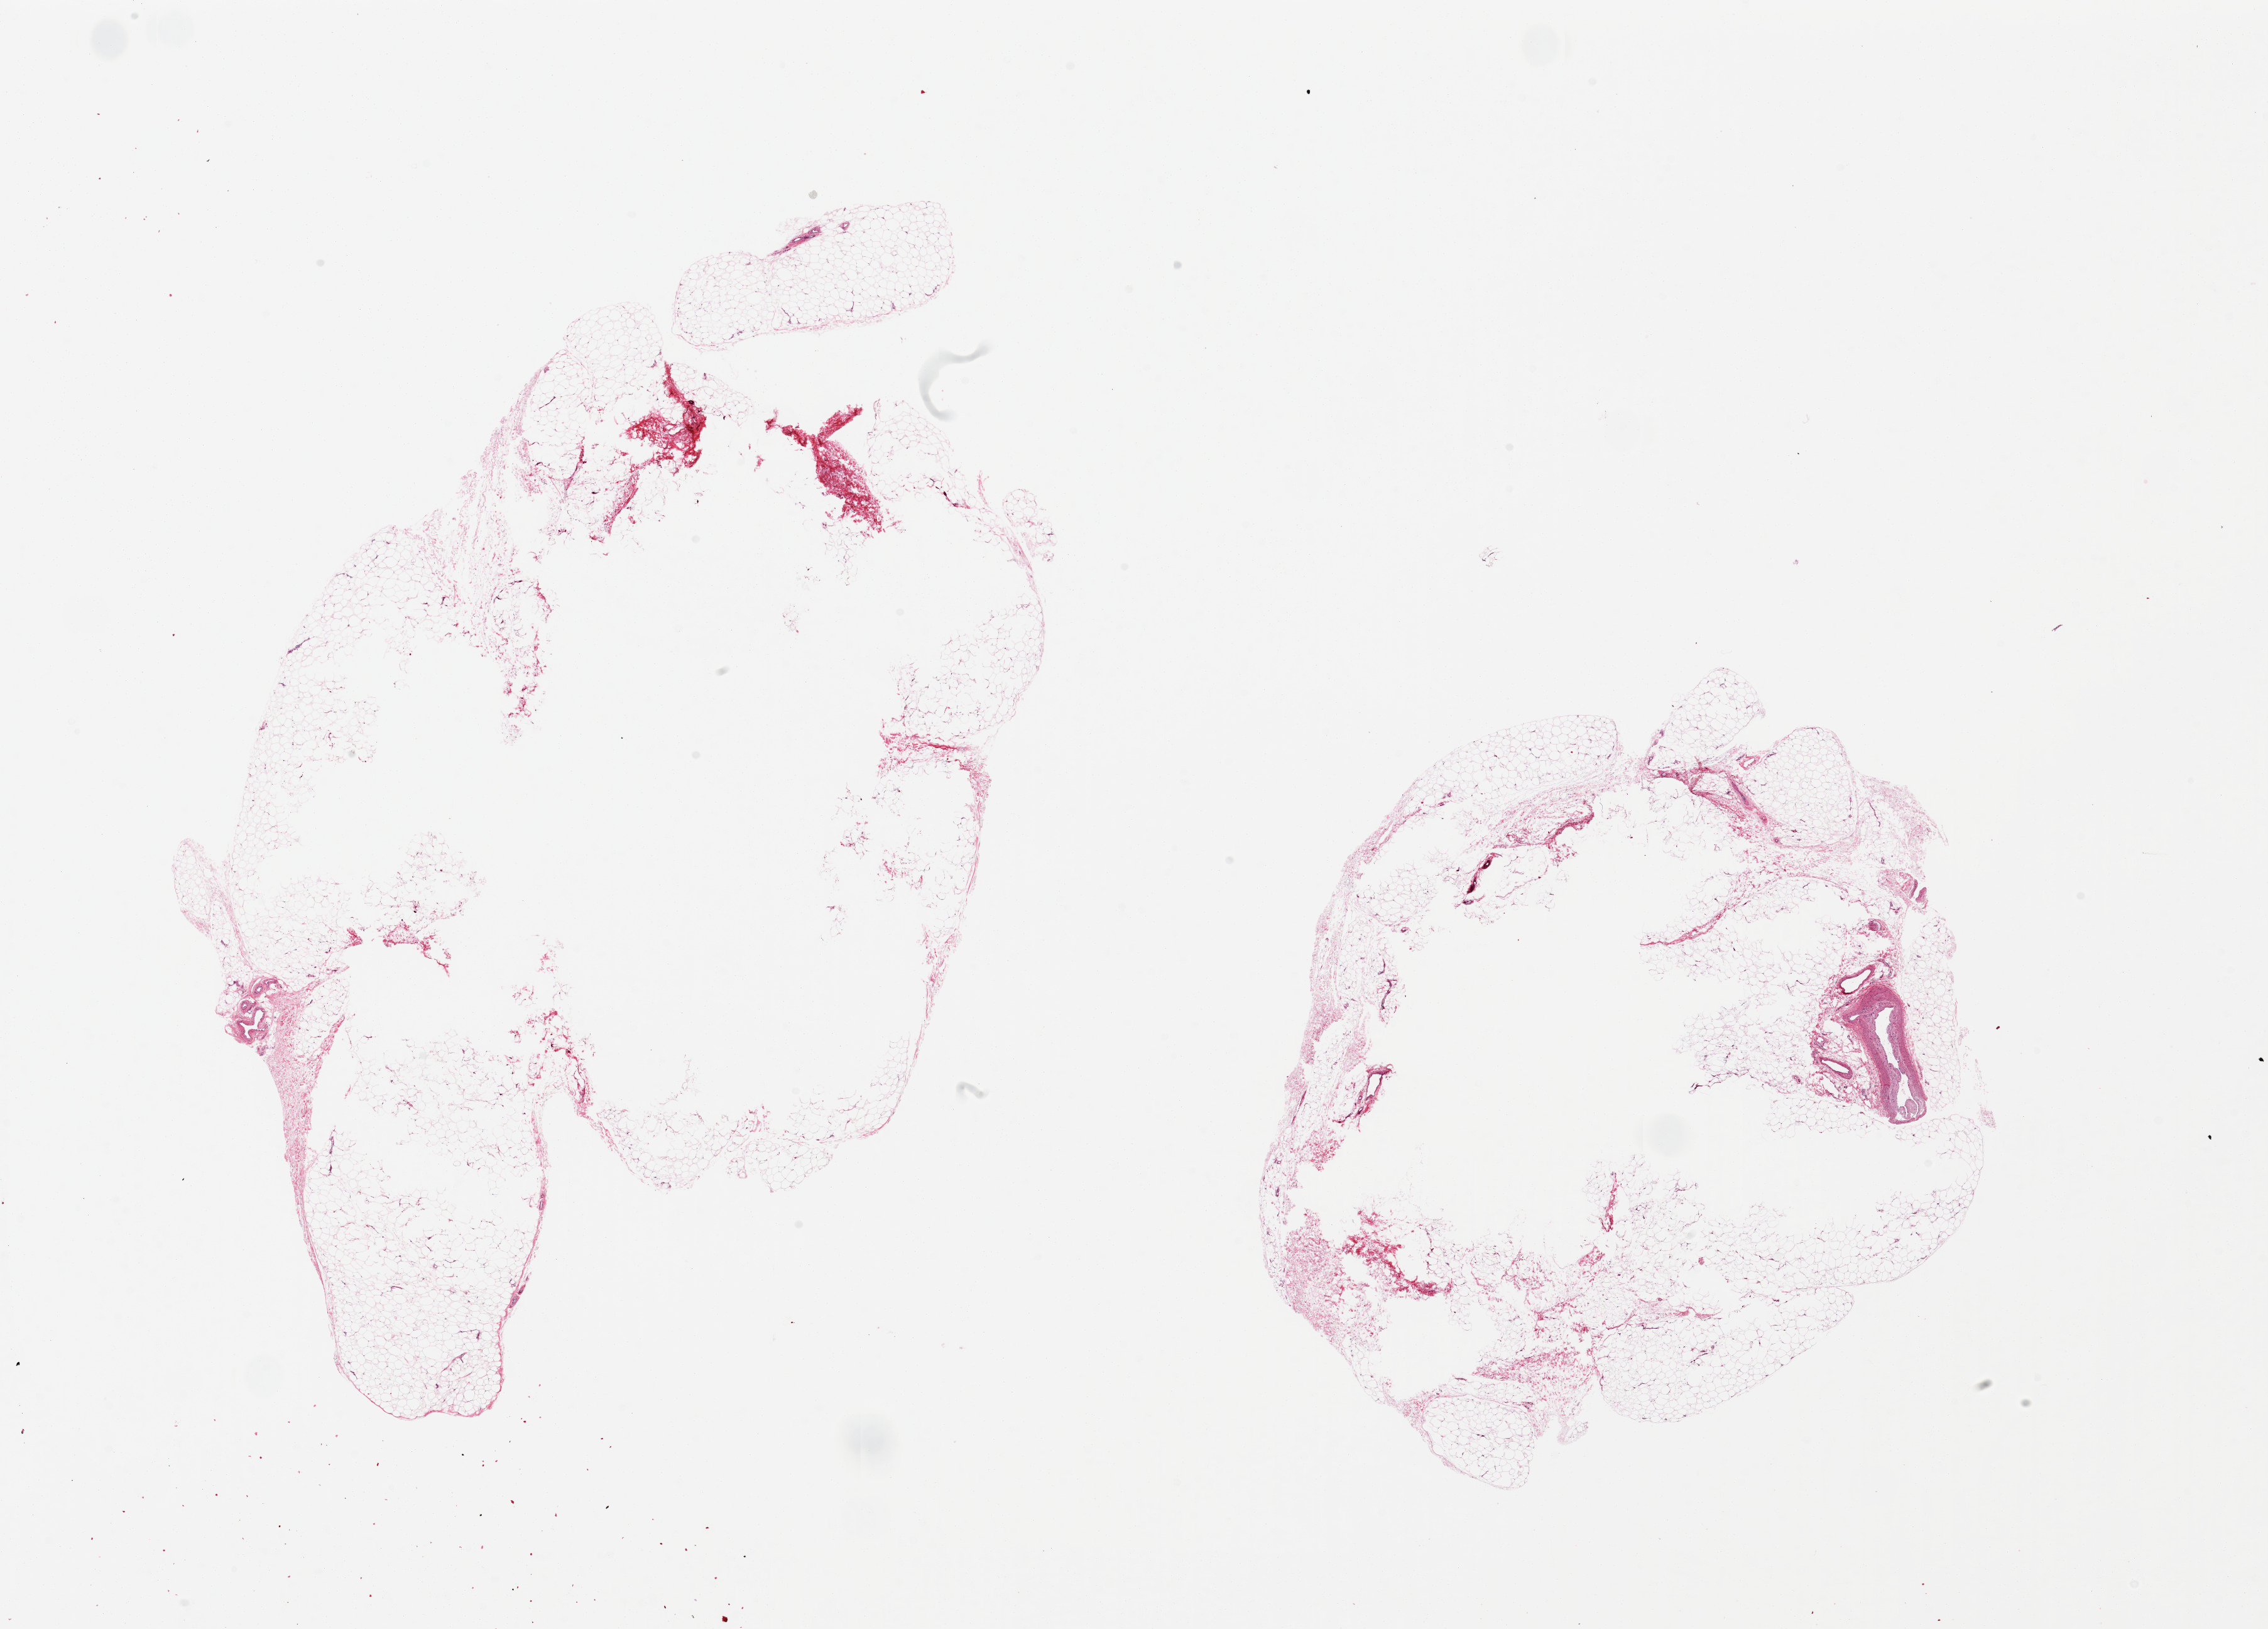
Digitized hematoxylin and eosin (H&E)-stained section, shown as a low-resolution overview of the whole scanned area (about 28.5 x 20.5 mm). PAXgene-fixed paraffin-embedded (PFPE) section. Target tissue: adipose tissue. Donor tissue sample. Donor sex: male.
Reviewer comment on this tissue sample: 2 pieces, 16.7x9 & 10.7x8.6 mm; large central holes in both (inadequate fixation); only outer ~1.5 mm preserved for molecular studies.